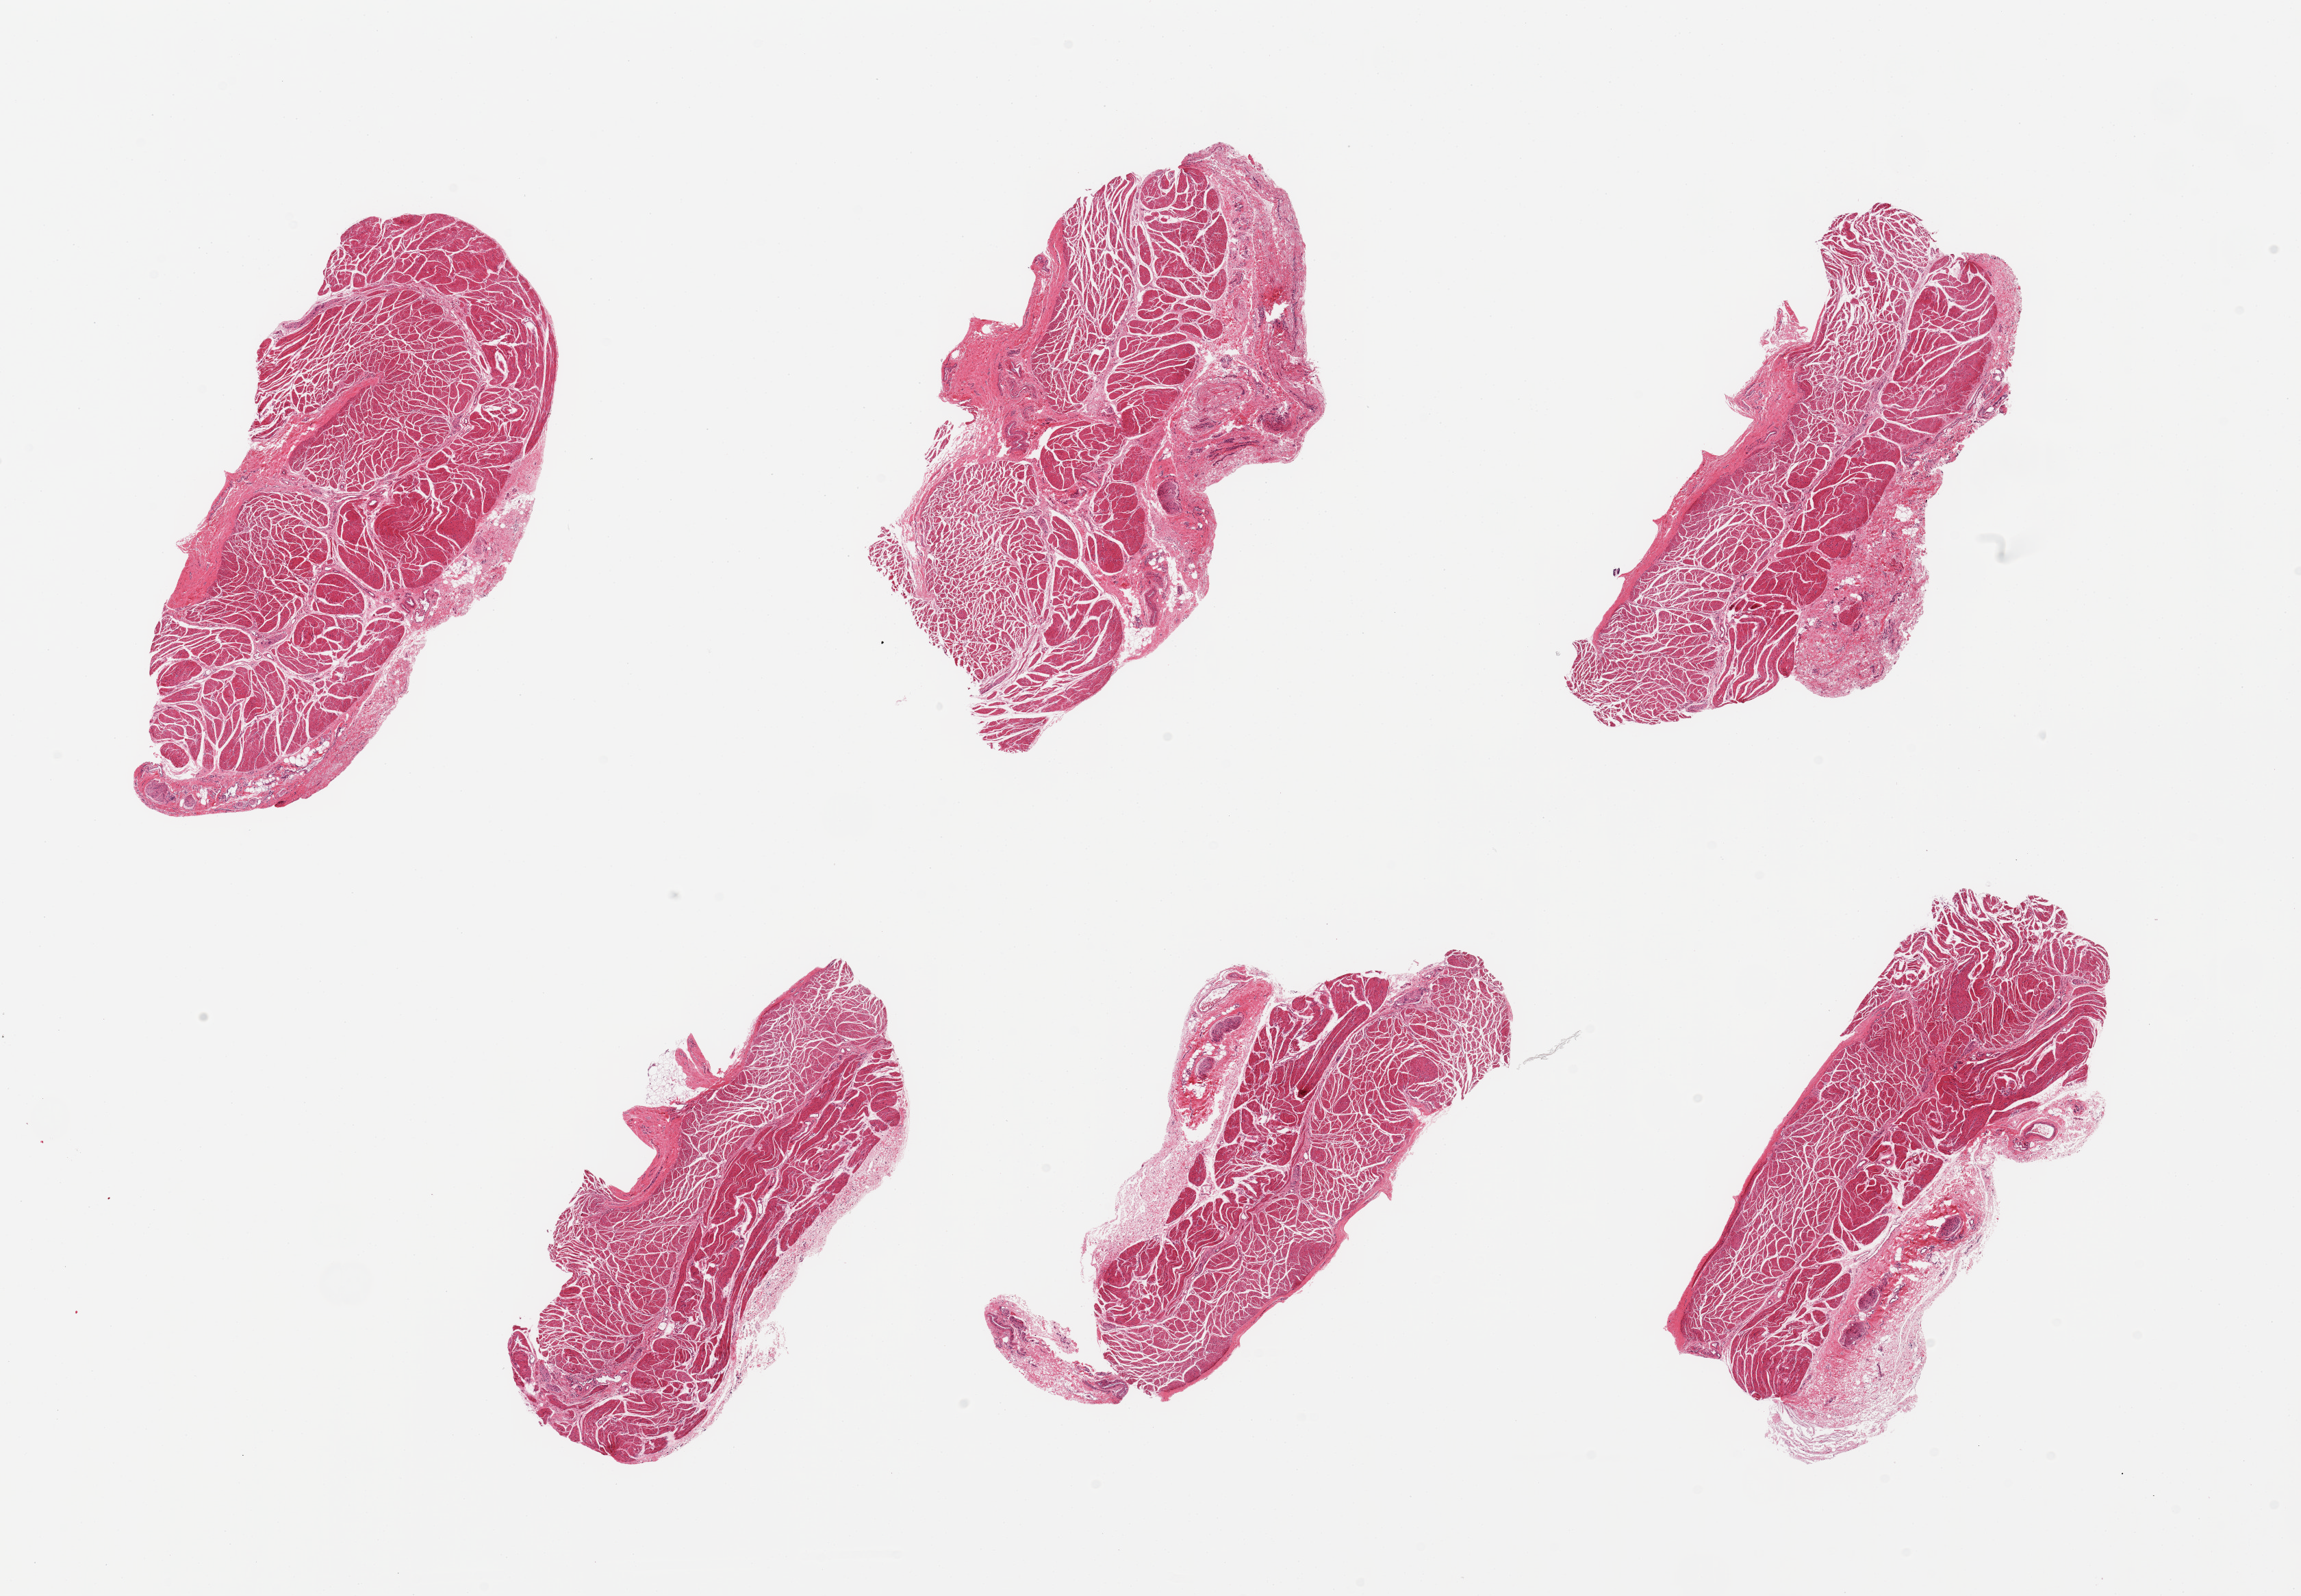
H&E whole-slide image, a low-resolution overview of the entire scanned area, about 26.6 x 18.4 mm (from a 20x scan). PAXgene-fixed paraffin-embedded (PFPE) section. Section of esophageal muscle (target tissue). Donor tissue sample. Female donor.
Pathologist's review note for this sample: 6 pieces; well dissected.